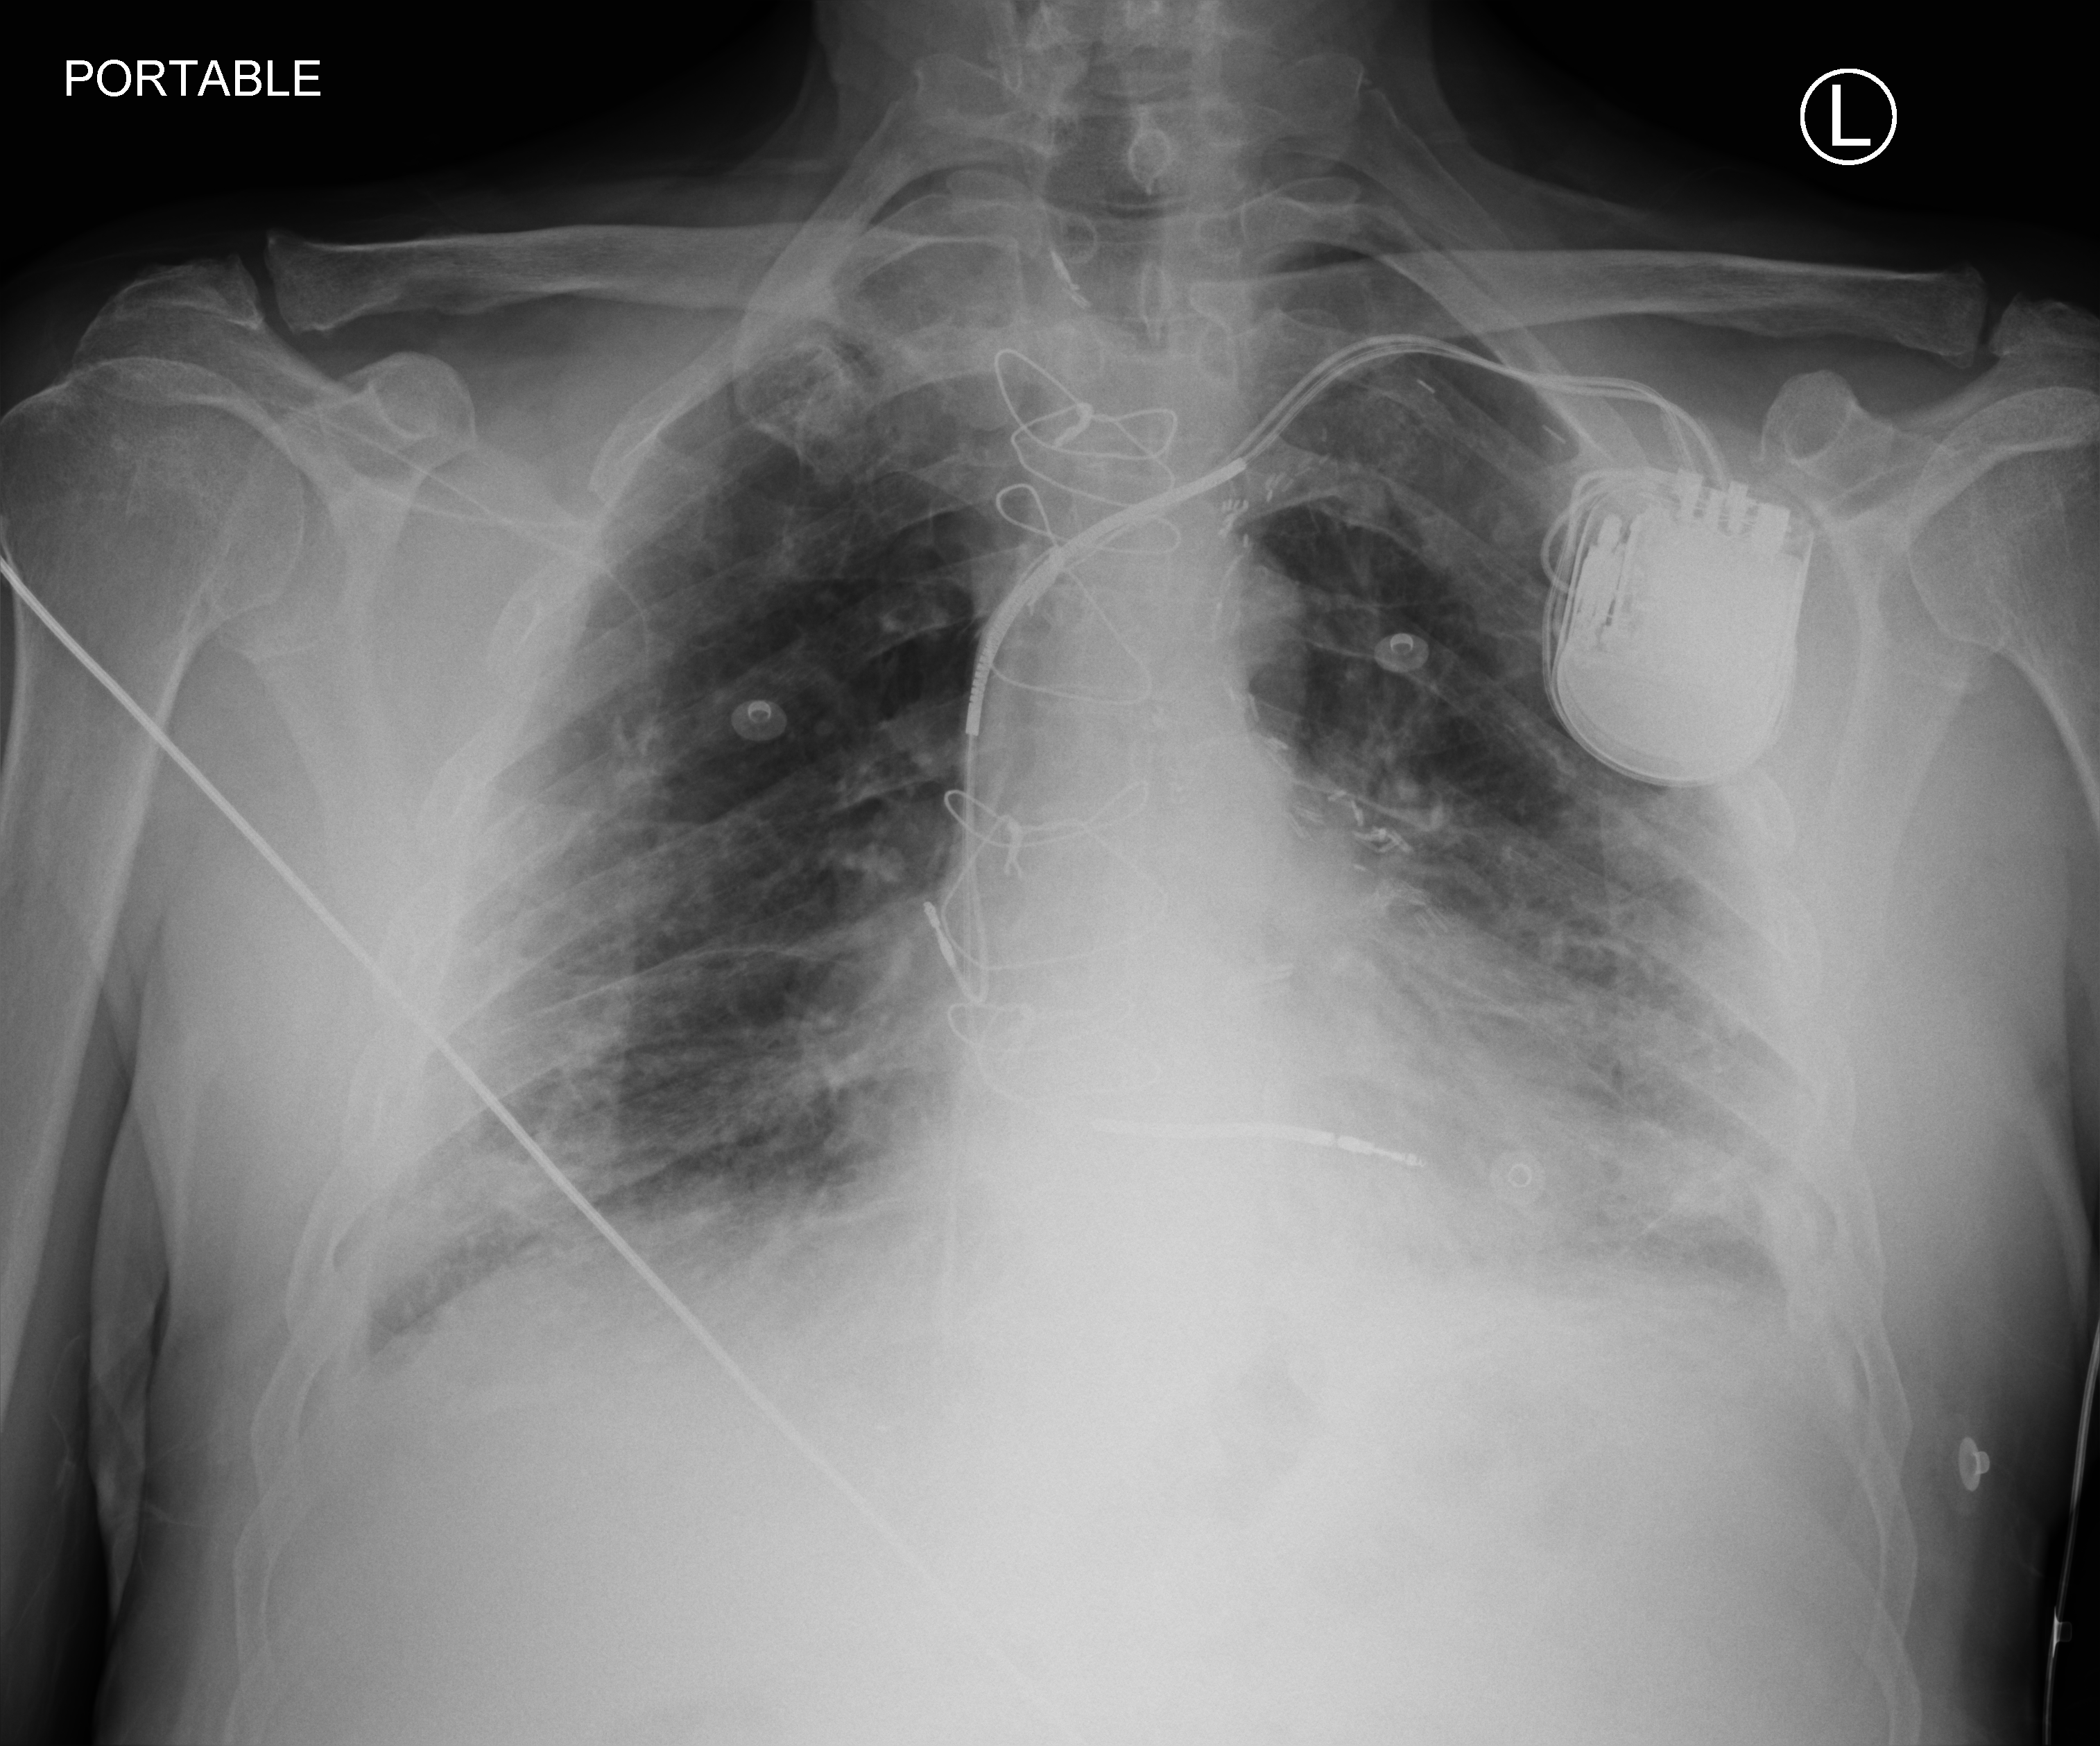
Bedside chest radiograph (computed radiography); anteroposterior (AP) projection. Patient hospitalised with COVID-19; male, aged 75–90 years.
From the hospital-stay record, not from the radiograph (when in the stay this image was taken is not recorded):
- mechanically ventilated during this hospital stay: no
- chronic kidney disease (admission record): no